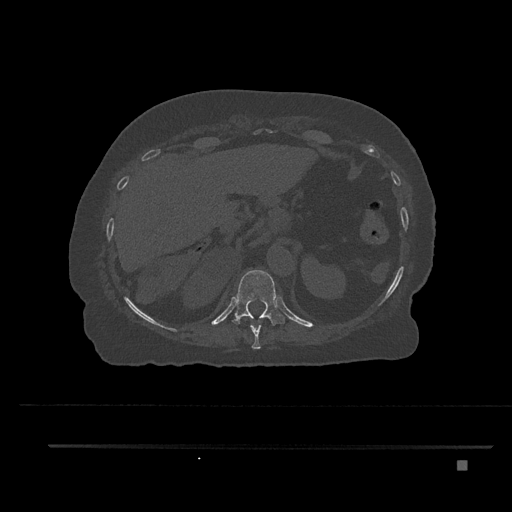
CT including the spine, one axial slice; slice 323 of 797 in the series (ordered by position); reconstruction kernel Br40s/3; 120 kVp; bone window (W 1800 / L 400 HU); 0.5 mm slice thickness; 512 × 512 image matrix, field of view 437 × 437 mm. Patient: female, 76 years. From the clinical record (not read from this slice): primary cancer: lung; vertebrae with lytic lesions (as recorded): T11, L3.
Structures marked on this image (semi-automatic segmentation, software-assisted and operator-edited):
- T10 vertebra: bounding box (x1, y1, x2, y2) in pixels: (243, 318, 261, 349)
- T11 vertebra: (233, 270, 285, 326)